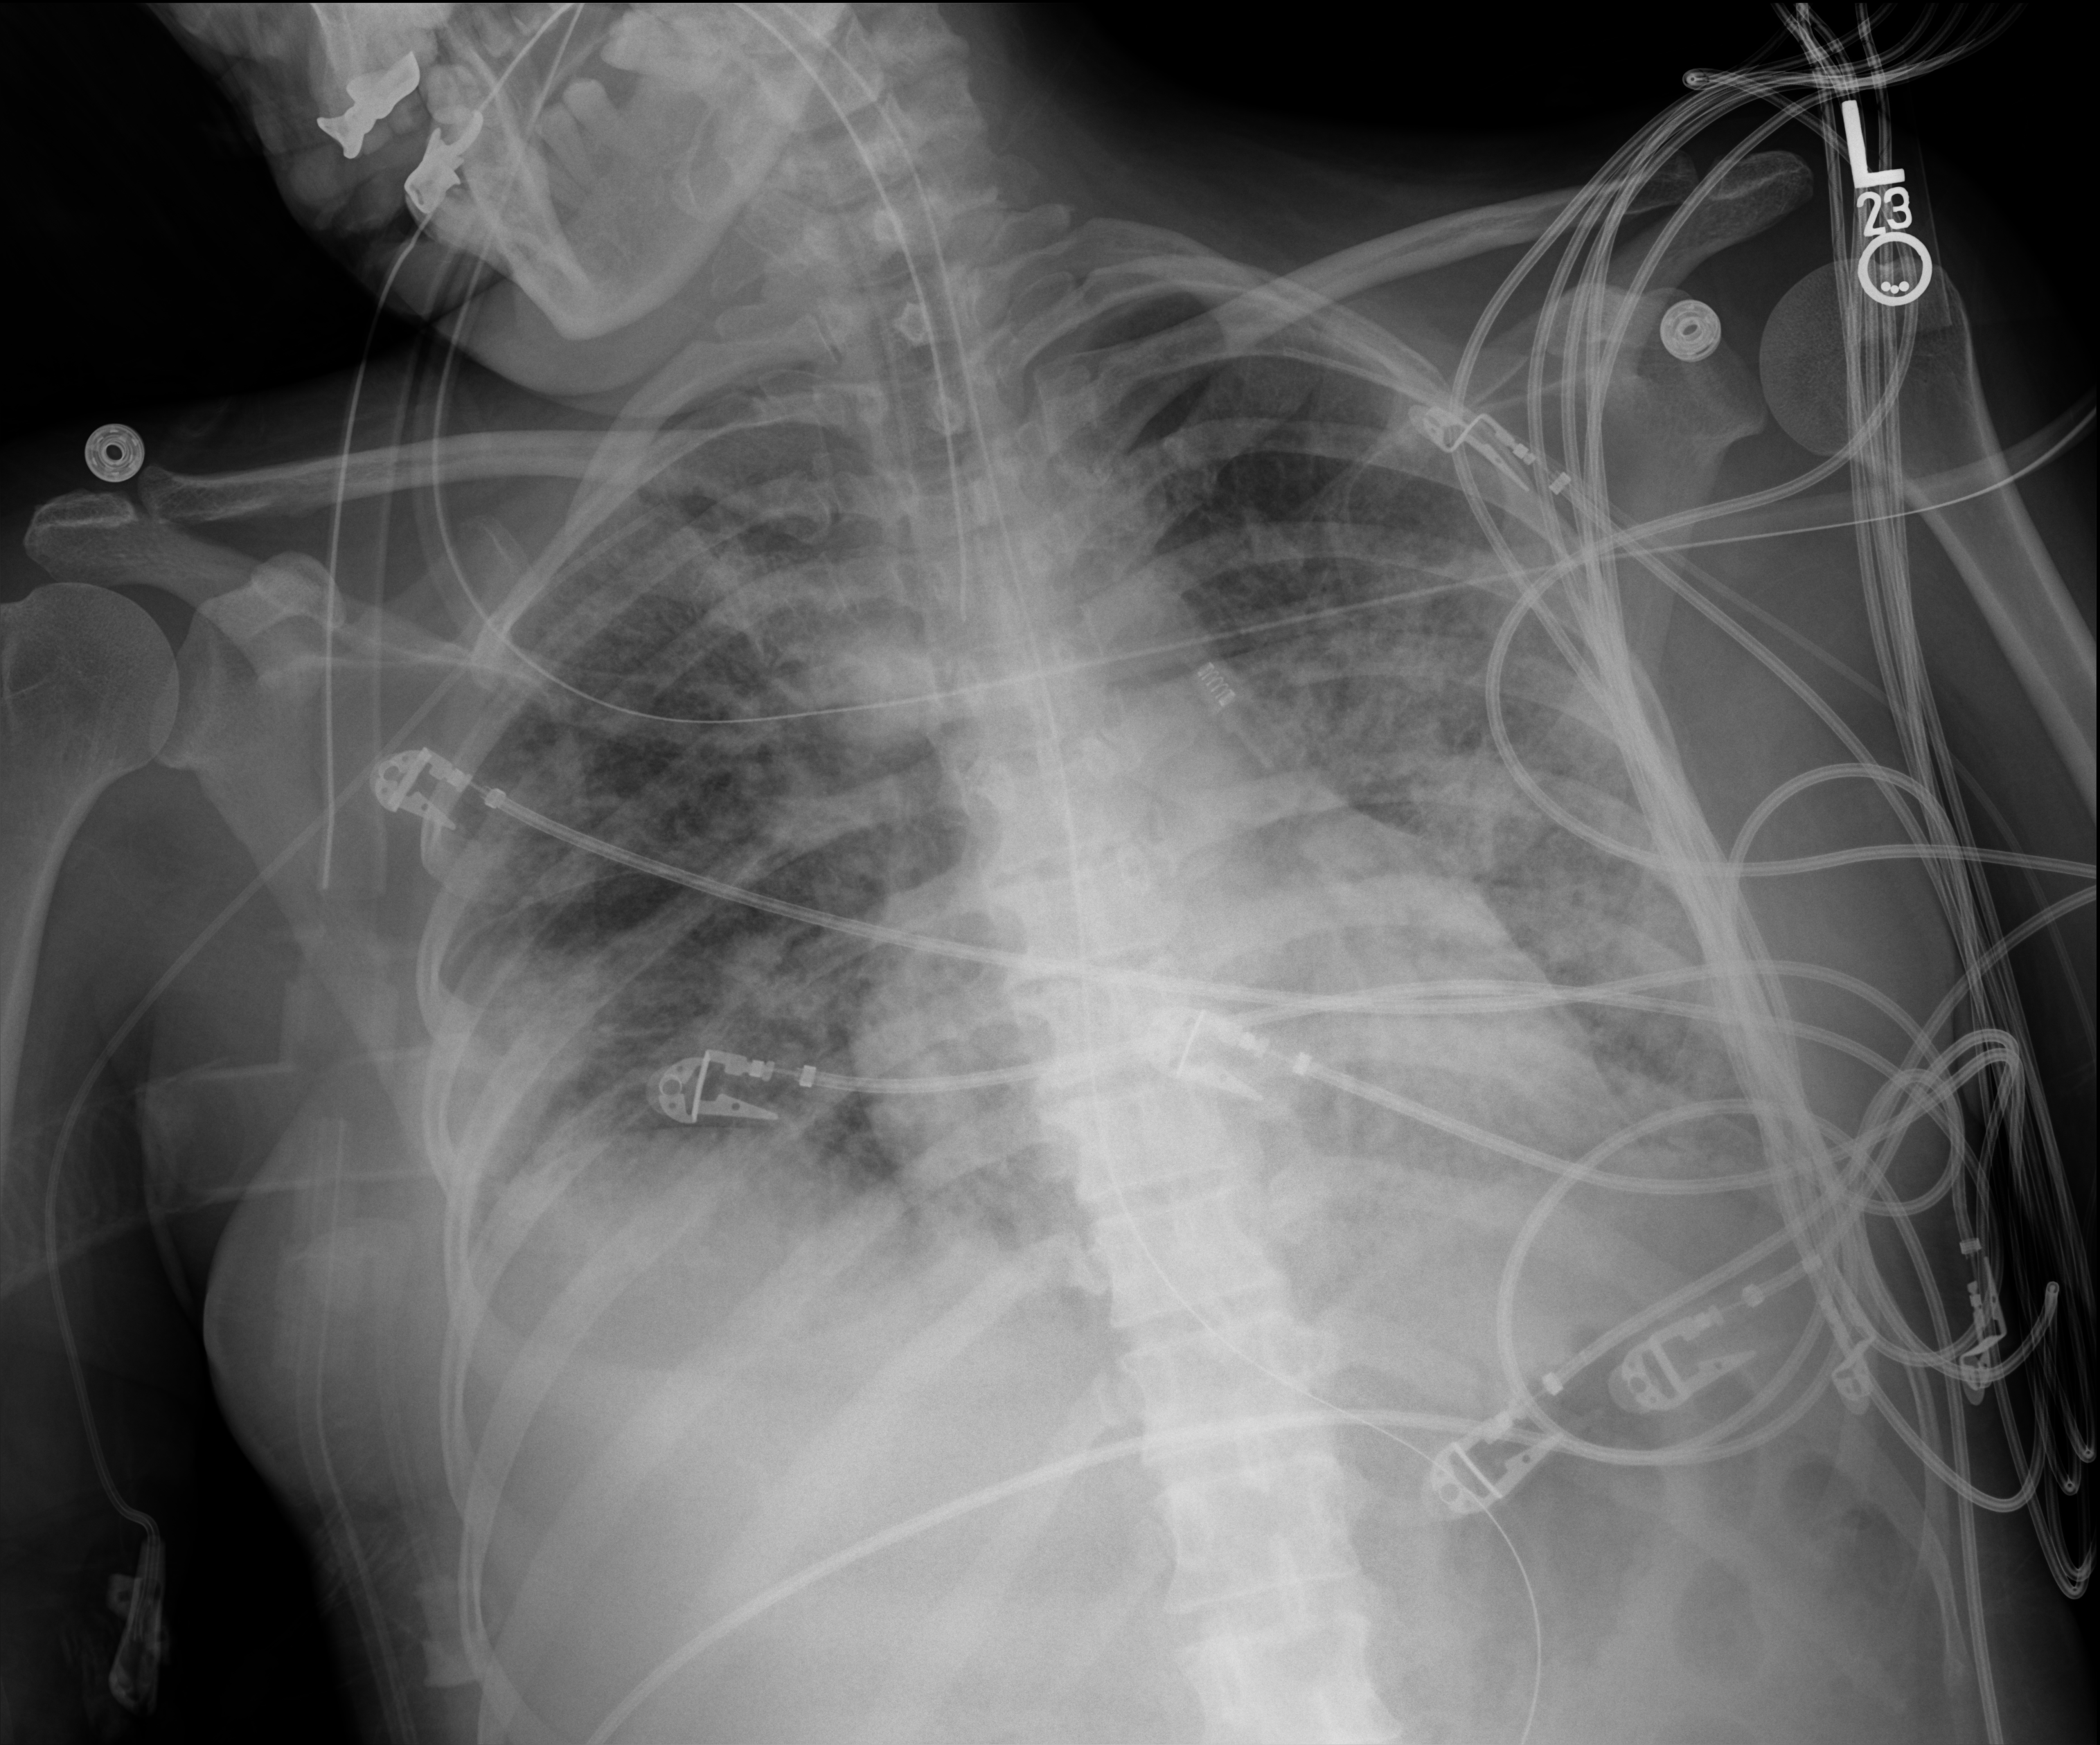
Chest X-ray (portable), anteroposterior (AP) projection. Patient hospitalised with COVID-19; female, aged 18–59 years.
Hospital-stay facts (about this admission, not read from this image; timing relative to this image not recorded): COPD (admission record): no; mechanically ventilated during this hospital stay: yes.